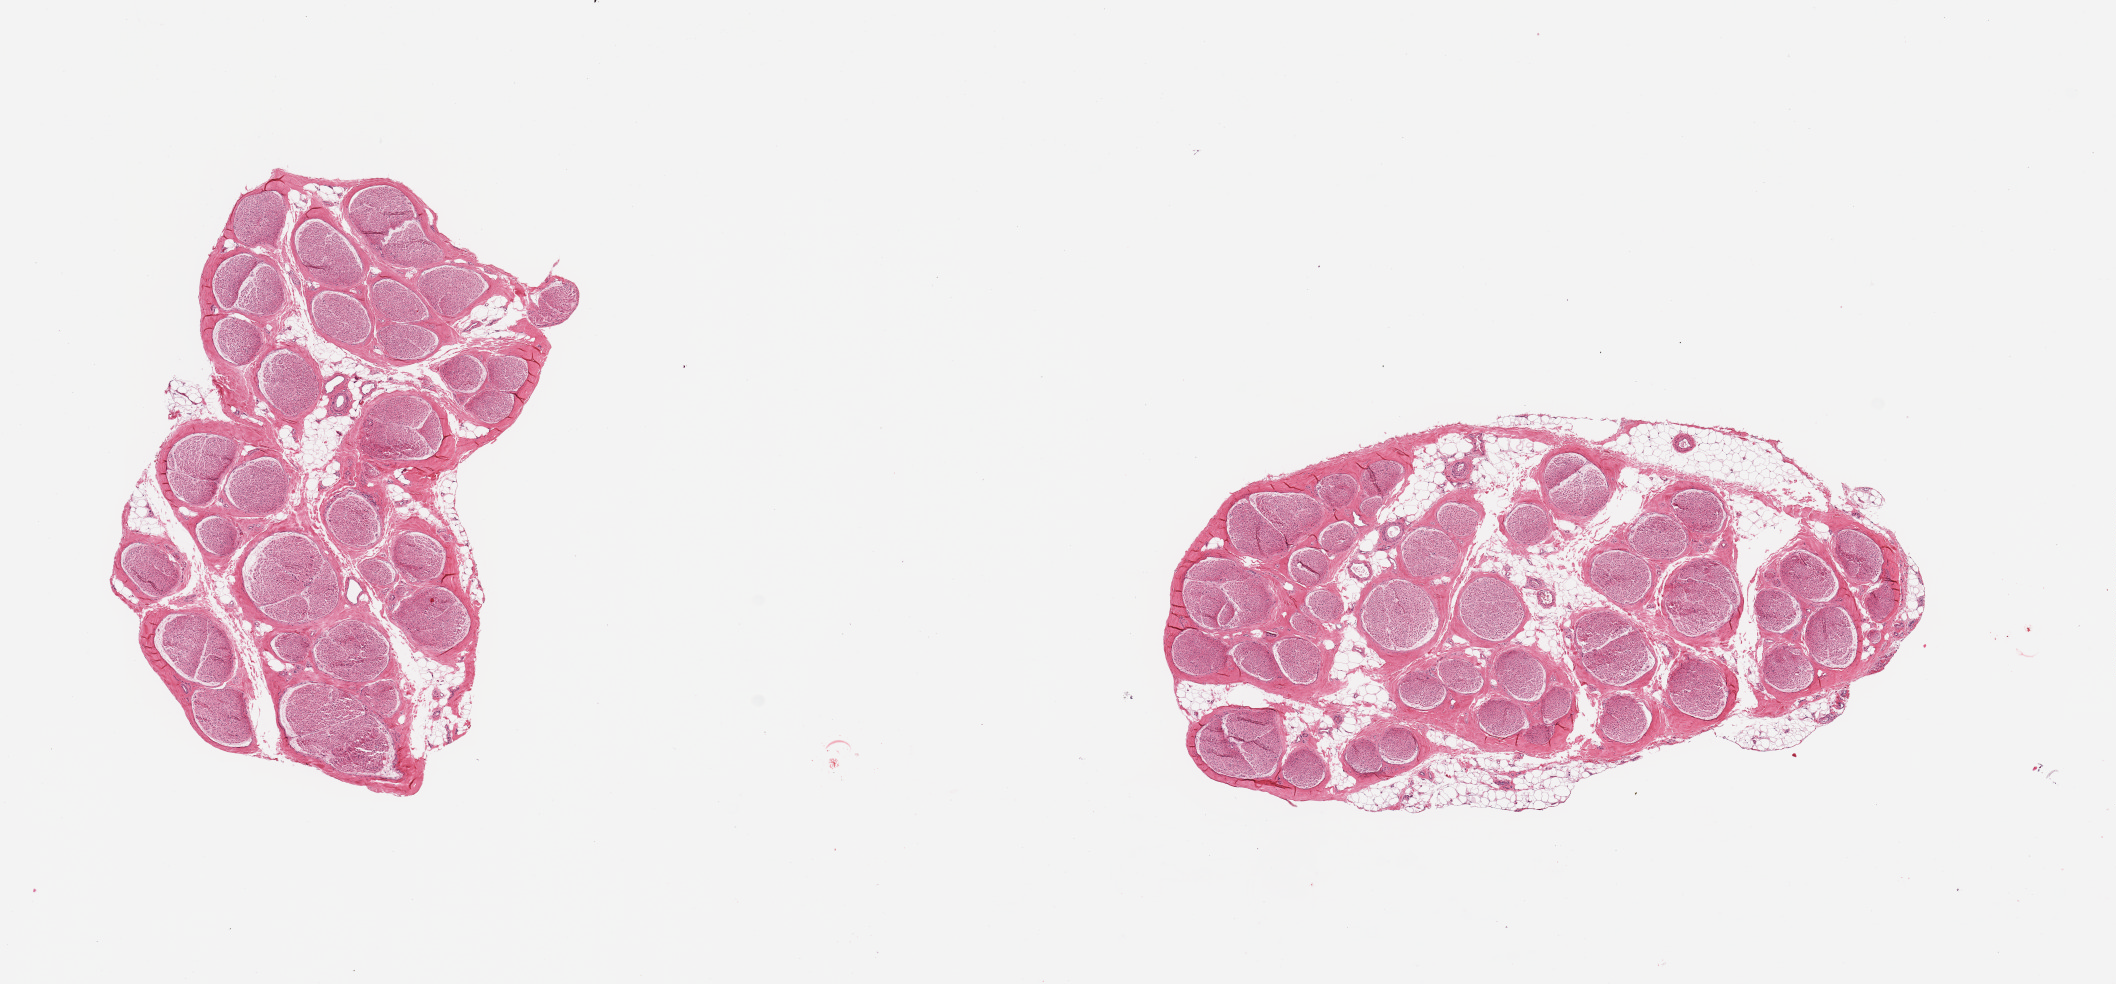
Hematoxylin and eosin (H&E) whole-slide image, brightfield, shown as a low-resolution overview of the whole scanned area (about 16.7 x 7.8 mm, acquisition: 20x scan). PAXgene-fixed paraffin-embedded (PFPE) section. Sampled site (target tissue): tibial nerve. Donor tissue sample.
Review note (as recorded): 2 pieces, neglibilbe adherent fat.